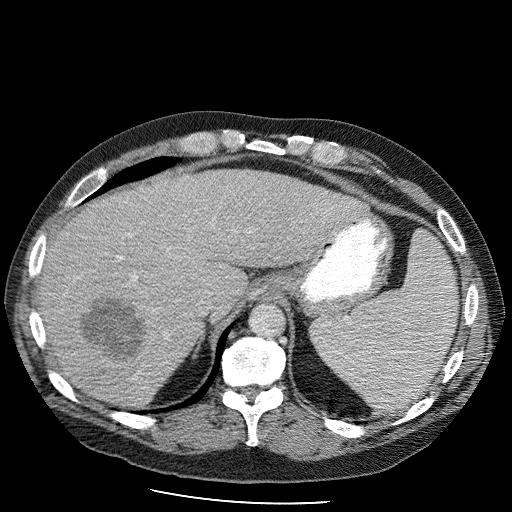
Contrast-enhanced abdominal CT (liver protocol), one axial slice; slice 77 of 98 in the series (ordered by position); reconstruction kernel STANDARD; 120 kVp; soft-tissue window (W 400 / L 40 HU); 2.5 mm slice thickness; 512 × 512 image matrix, field of view 400 × 400 mm. From the clinical record (not read from this slice): diagnosis: hepatocellular carcinoma (patient treated with transarterial chemoembolisation; whether this scan precedes or follows treatment is not stated here); TNM stage (as recorded): Stage-II; Child-Pugh class: B; tumour nodularity: uninodular.
Outlined on this slice (semi-automatically segmented with operator editing):
- liver parenchyma outside the tumour (the mass and vessels are separate outlines, so this box may not span the whole liver): box from (x=38, y=169) to (x=366, y=410) px
- mass: (x=75, y=292)–(x=151, y=364)